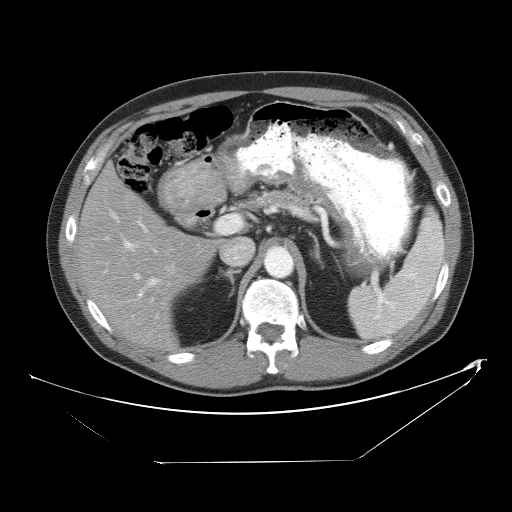
Contrast-enhanced abdominal CT, one axial slice; position 32 of 53 along the scan axis; reconstruction kernel STANDARD; intravenous contrast given; soft-tissue window (W 400 / L 40 HU); 5 mm slice thickness; 512 × 512 image matrix, field of view 438 × 438 mm. Male patient, age 59 years. Case-level facts recorded for this patient, not image findings: diagnosis: colorectal cancer liver metastases, imaged before liver resection; multiple liver metastases: yes; largest metastasis: 8.5 cm; disease in both lobes: no.
Outlined on this slice (manually delineated by an expert):
- hepatic veins: bounding box (x1, y1, x2, y2) in pixels: (106, 210, 158, 302)
- liver: (77, 167, 217, 351)
- planned liver remnant (the part of the liver to remain after resection): (77, 167, 217, 350)
- portal vein (with intrahepatic branches): (124, 216, 241, 297)